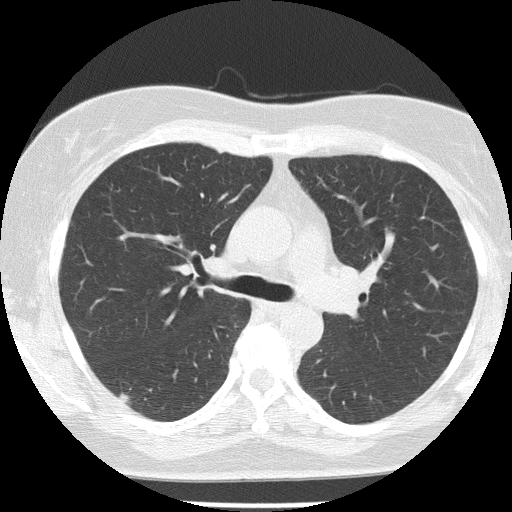
Axial slice from a low-dose chest CT screening exam; baseline screening round; lung window (W 1500 / L -600 HU); 512 × 512 image matrix. Female participant, aged 58 years at enrolment.
Lesion marked by an expert reader, bounding box [x1, y1, x2, y2] px = [100, 378, 150, 423]. The screening reader recorded 2 non-calcified nodules or masses ≥4 mm on this exam; which of them this box marks is not recorded. Official screen result: positive, change unspecified: nodule(s) >= 4 mm or enlarging nodule(s), mass(es), or other non-specific abnormalities suspicious for lung cancer. Lung cancer was diagnosed 648 days after this screen: adenocarcinoma, NOS, right lower lobe, well differentiated (G1), stage IB (AJCC 6th edition), 10 mm at pathology.